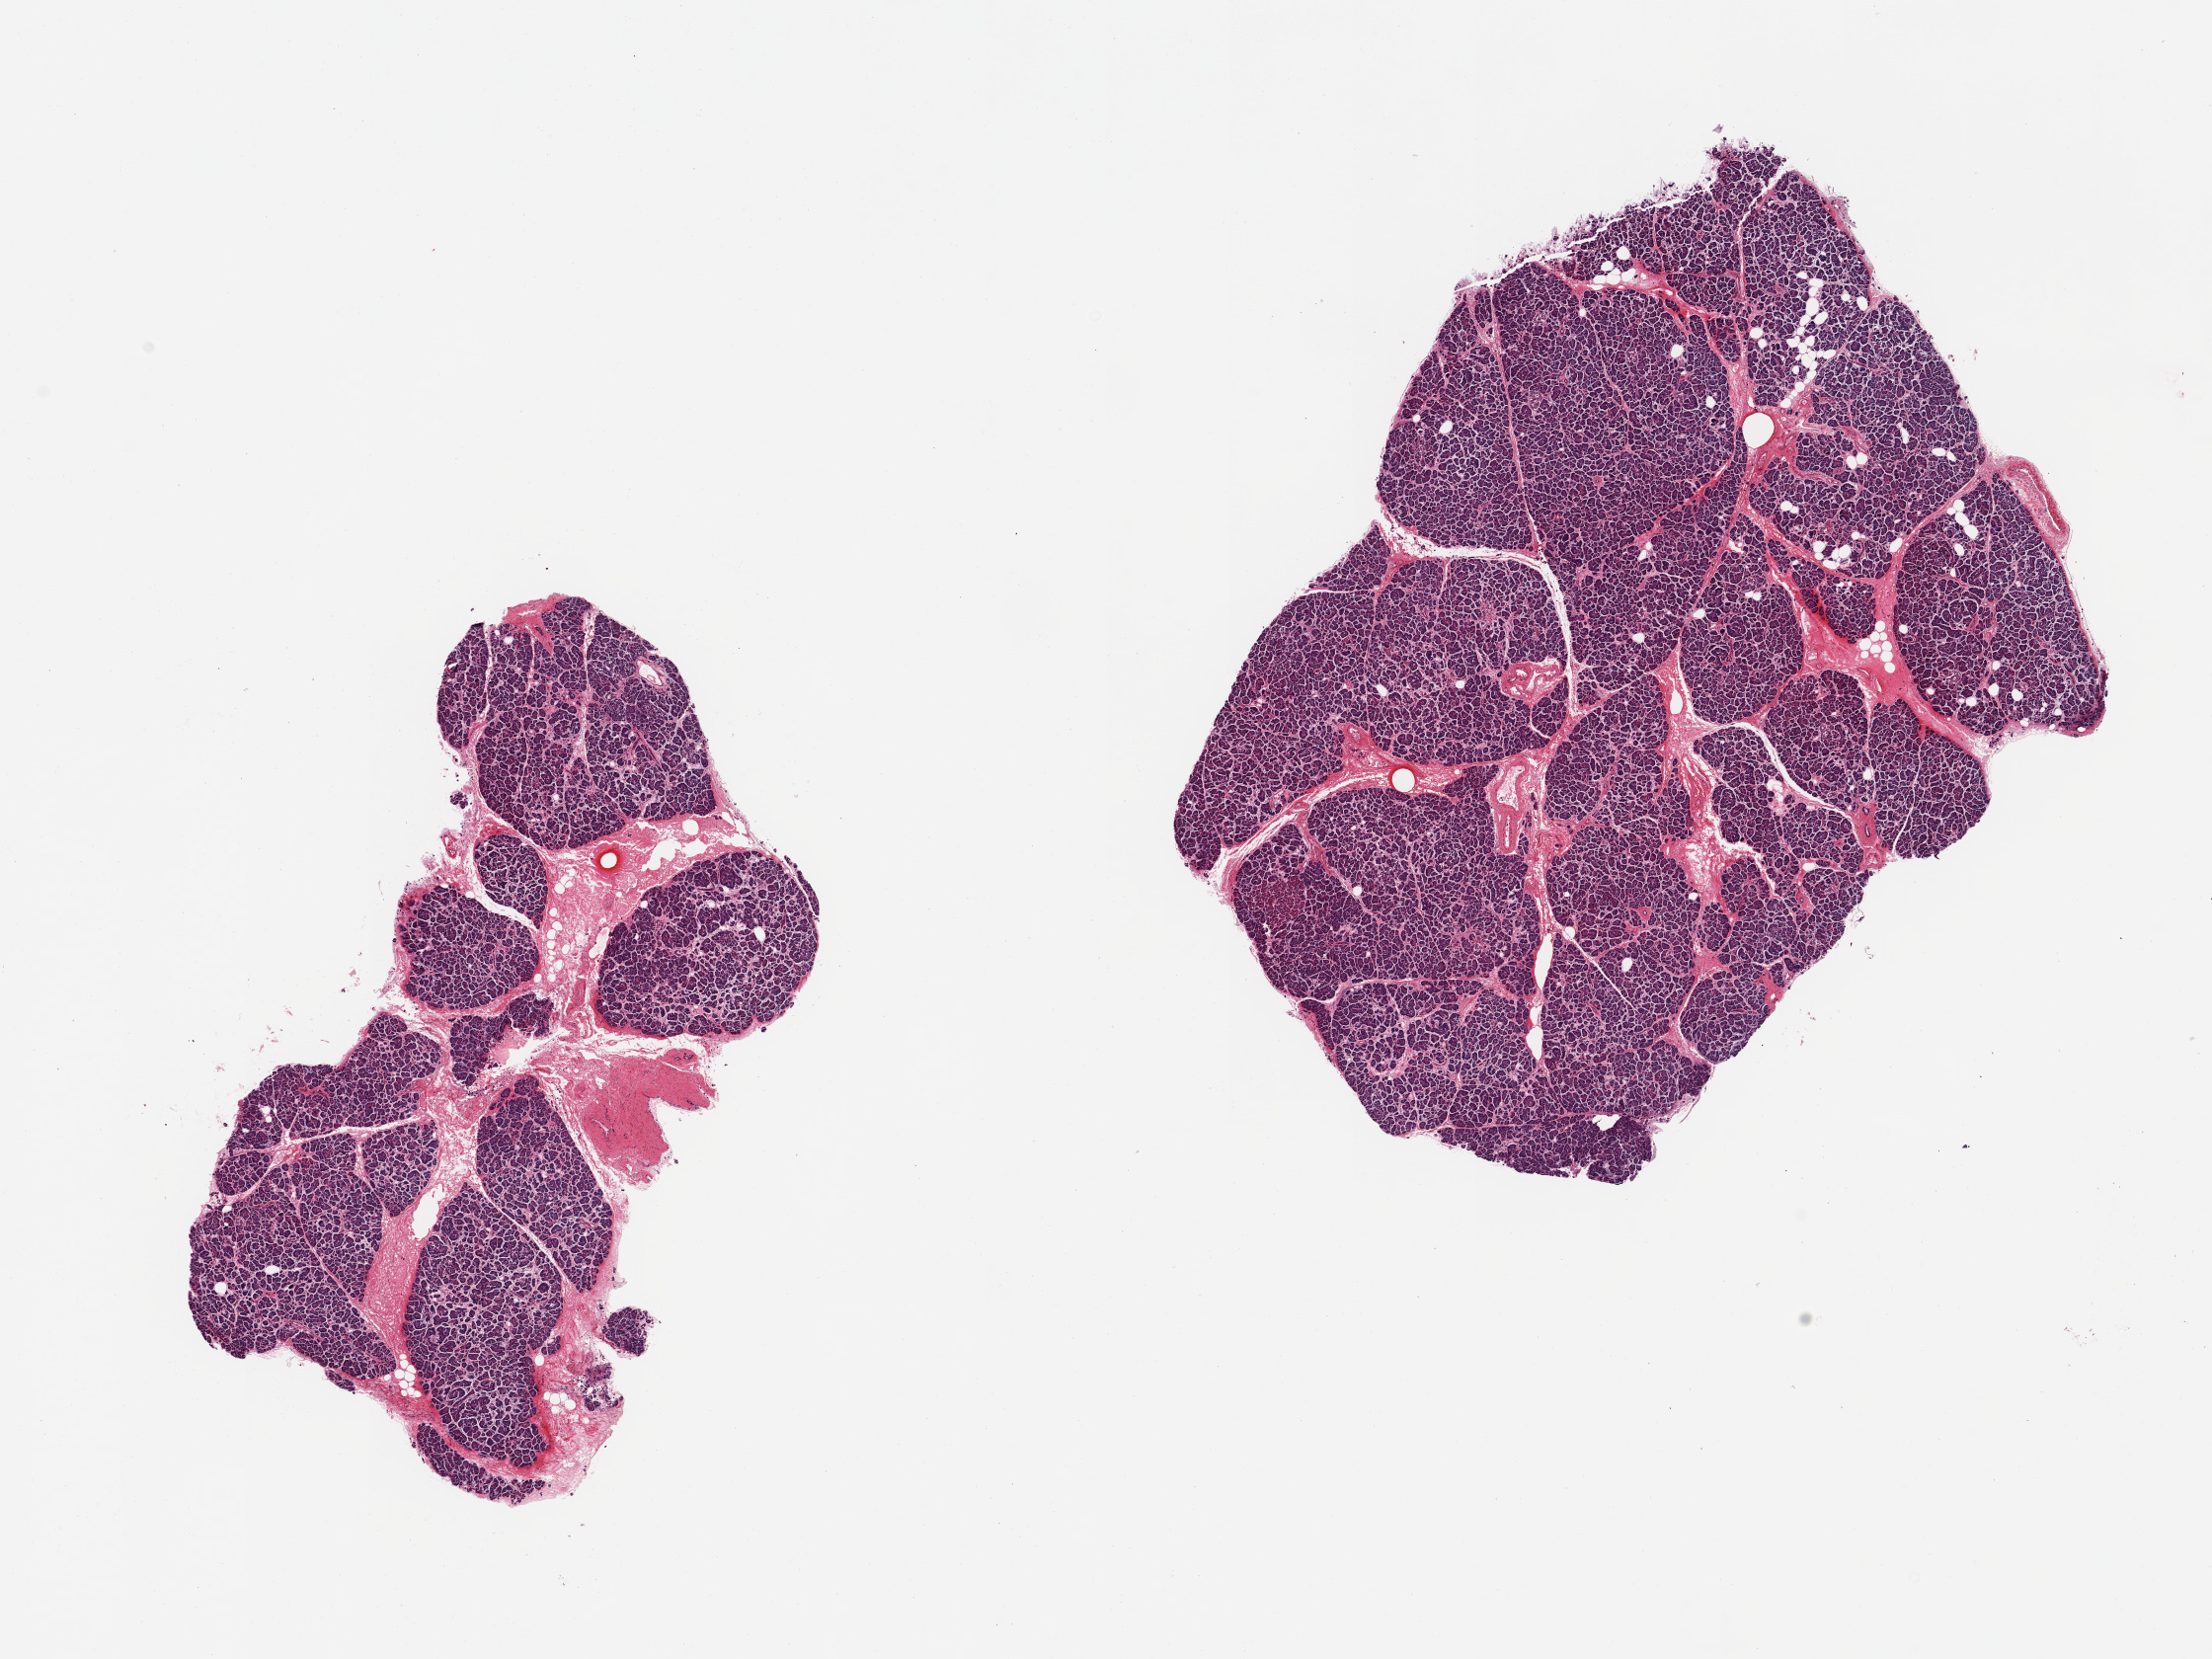
Hematoxylin and eosin (H&E) whole-slide image — a low-resolution overview of the entire scanned area, about 17.7 x 13.3 mm; PAXgene-fixed, paraffin-embedded tissue; target tissue: pancreas; donor tissue sample.
• pathologist's review note for this sample: 2 pieces; well trimmed